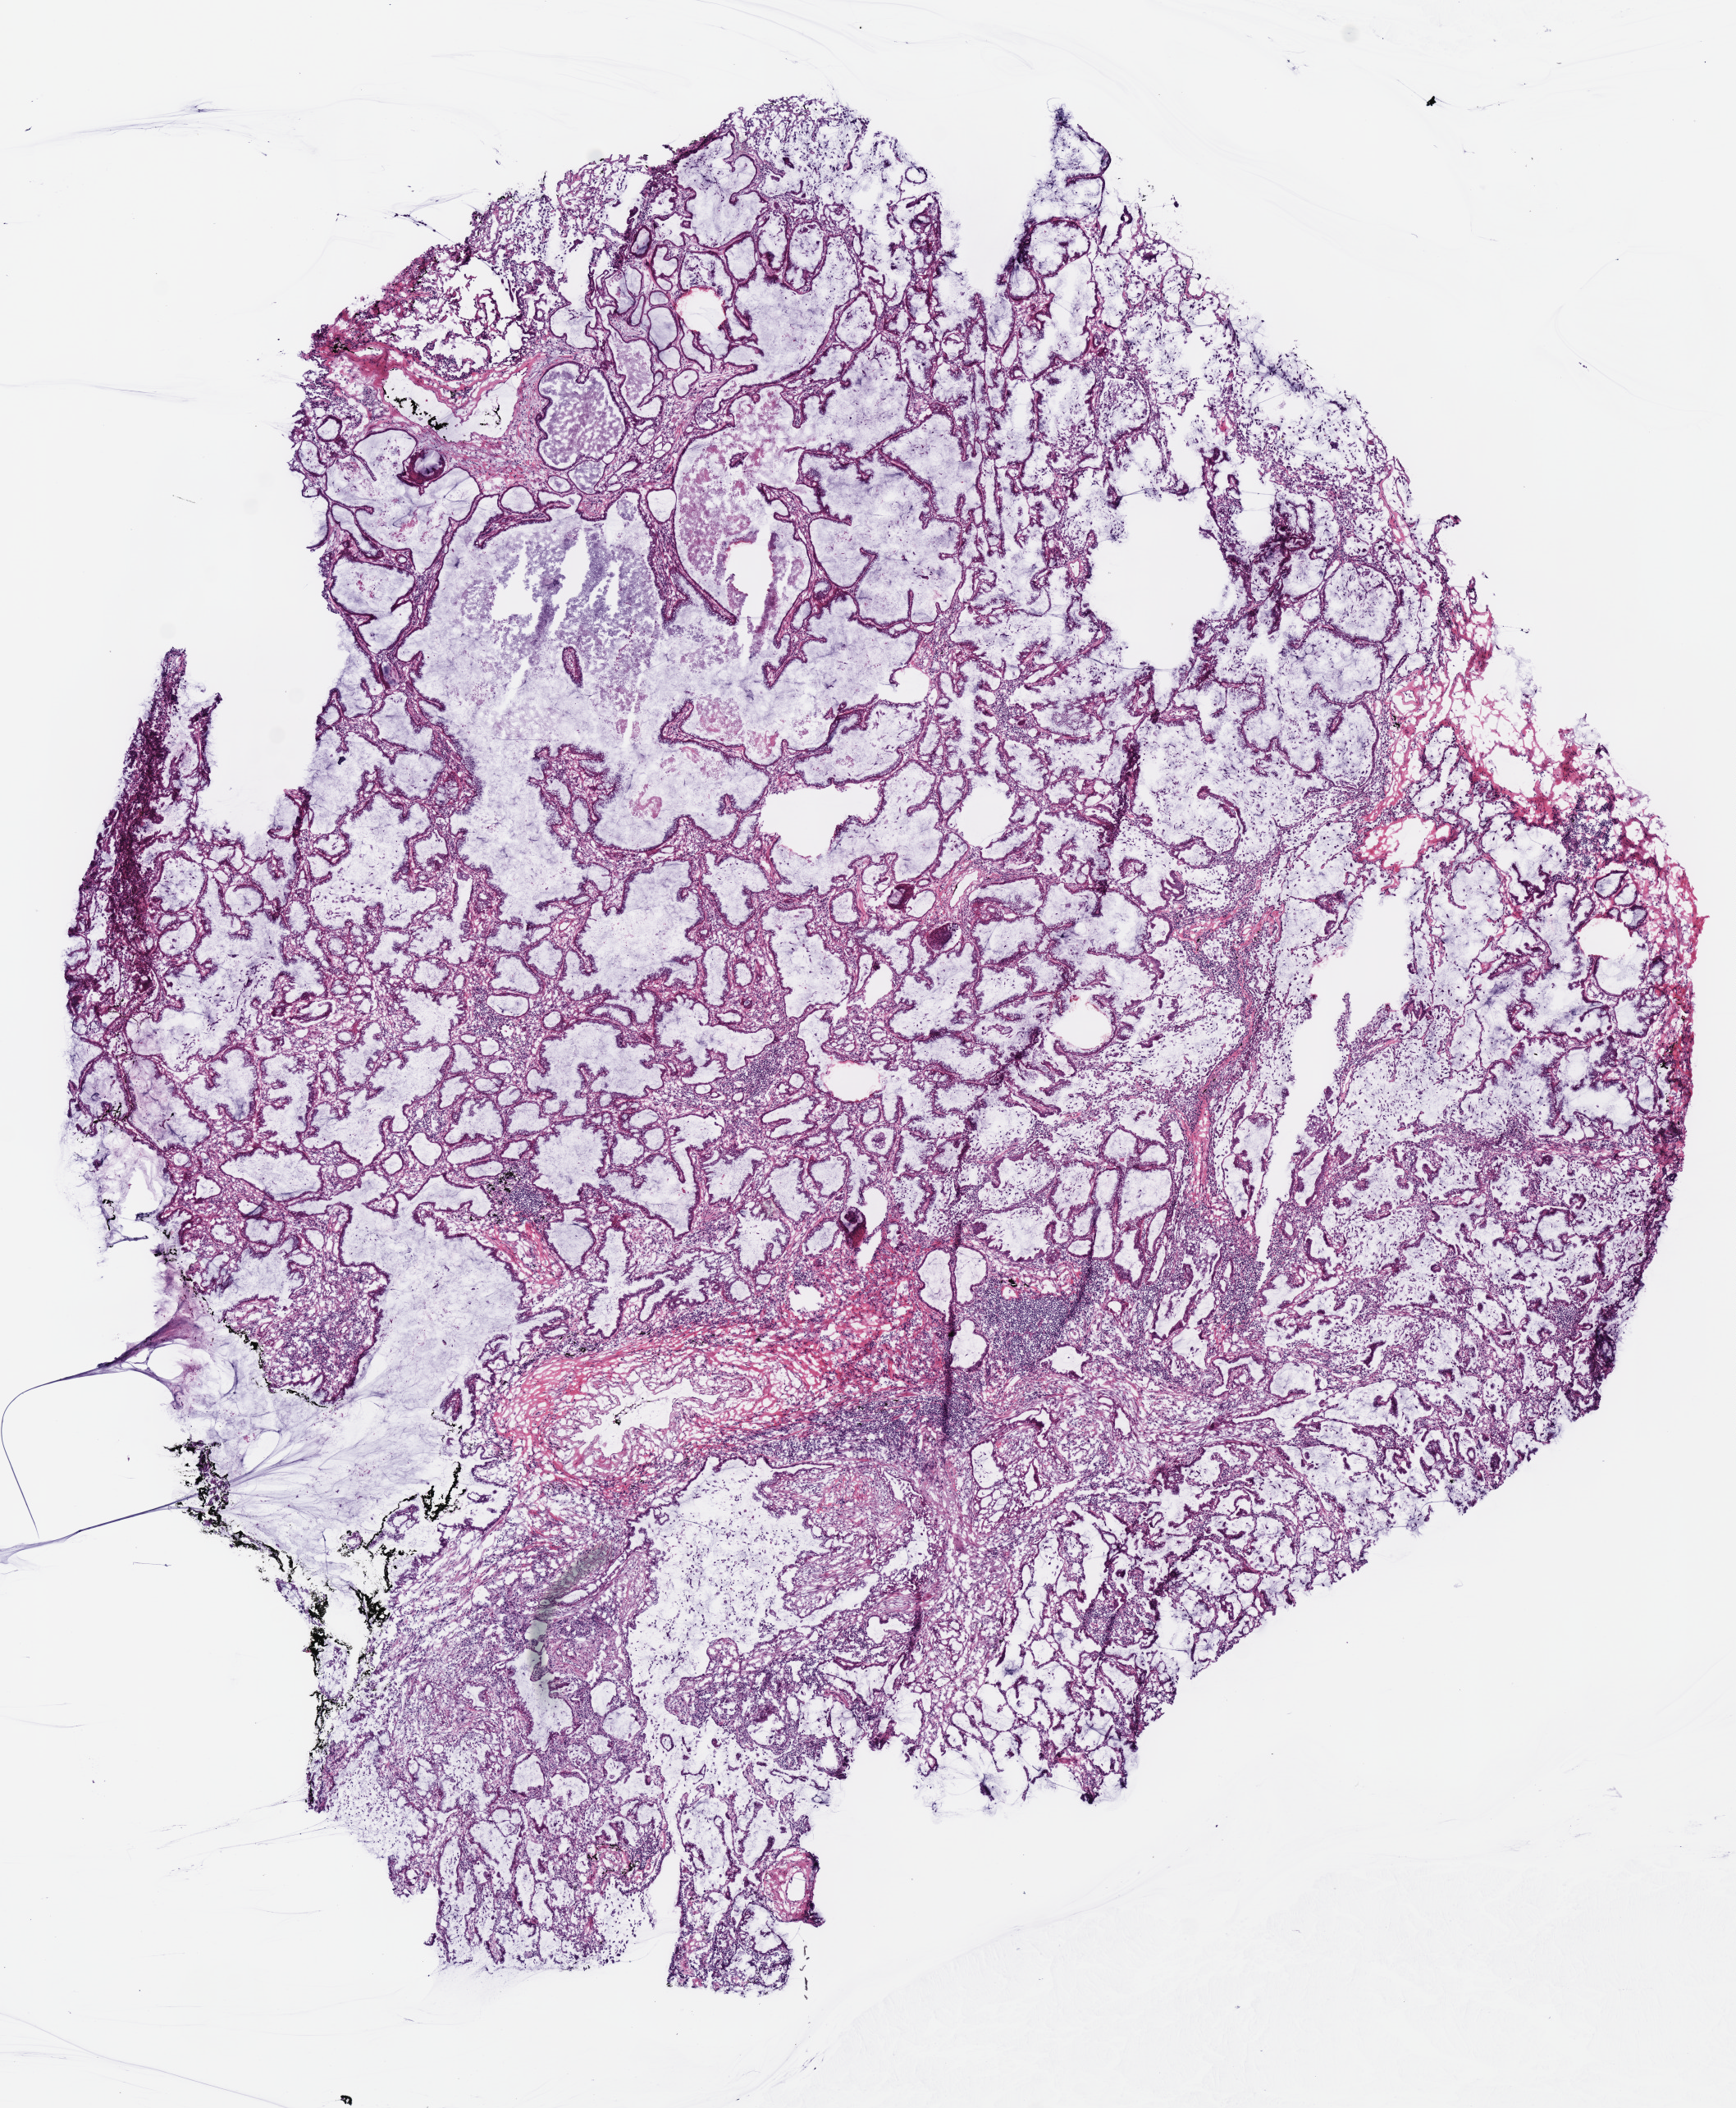
Whole-slide histology image, H&E, shown as a low-resolution overview of the whole scanned area (about 8.3 x 10.1 mm). Frozen section from the bottom of the tissue portion. Primary tumour sample from the lung. Patient: female, age at initial diagnosis 64 years. Composition of this section per pathologist review: tumour cells 85%, tumour nuclei 60%, normal cells 0%, stromal cells 15%, necrosis 0%.
Histologic diagnosis: Mucinous adenocarcinoma (upper lobe, lung). Laterality: left. AJCC pathologic stage: IB.